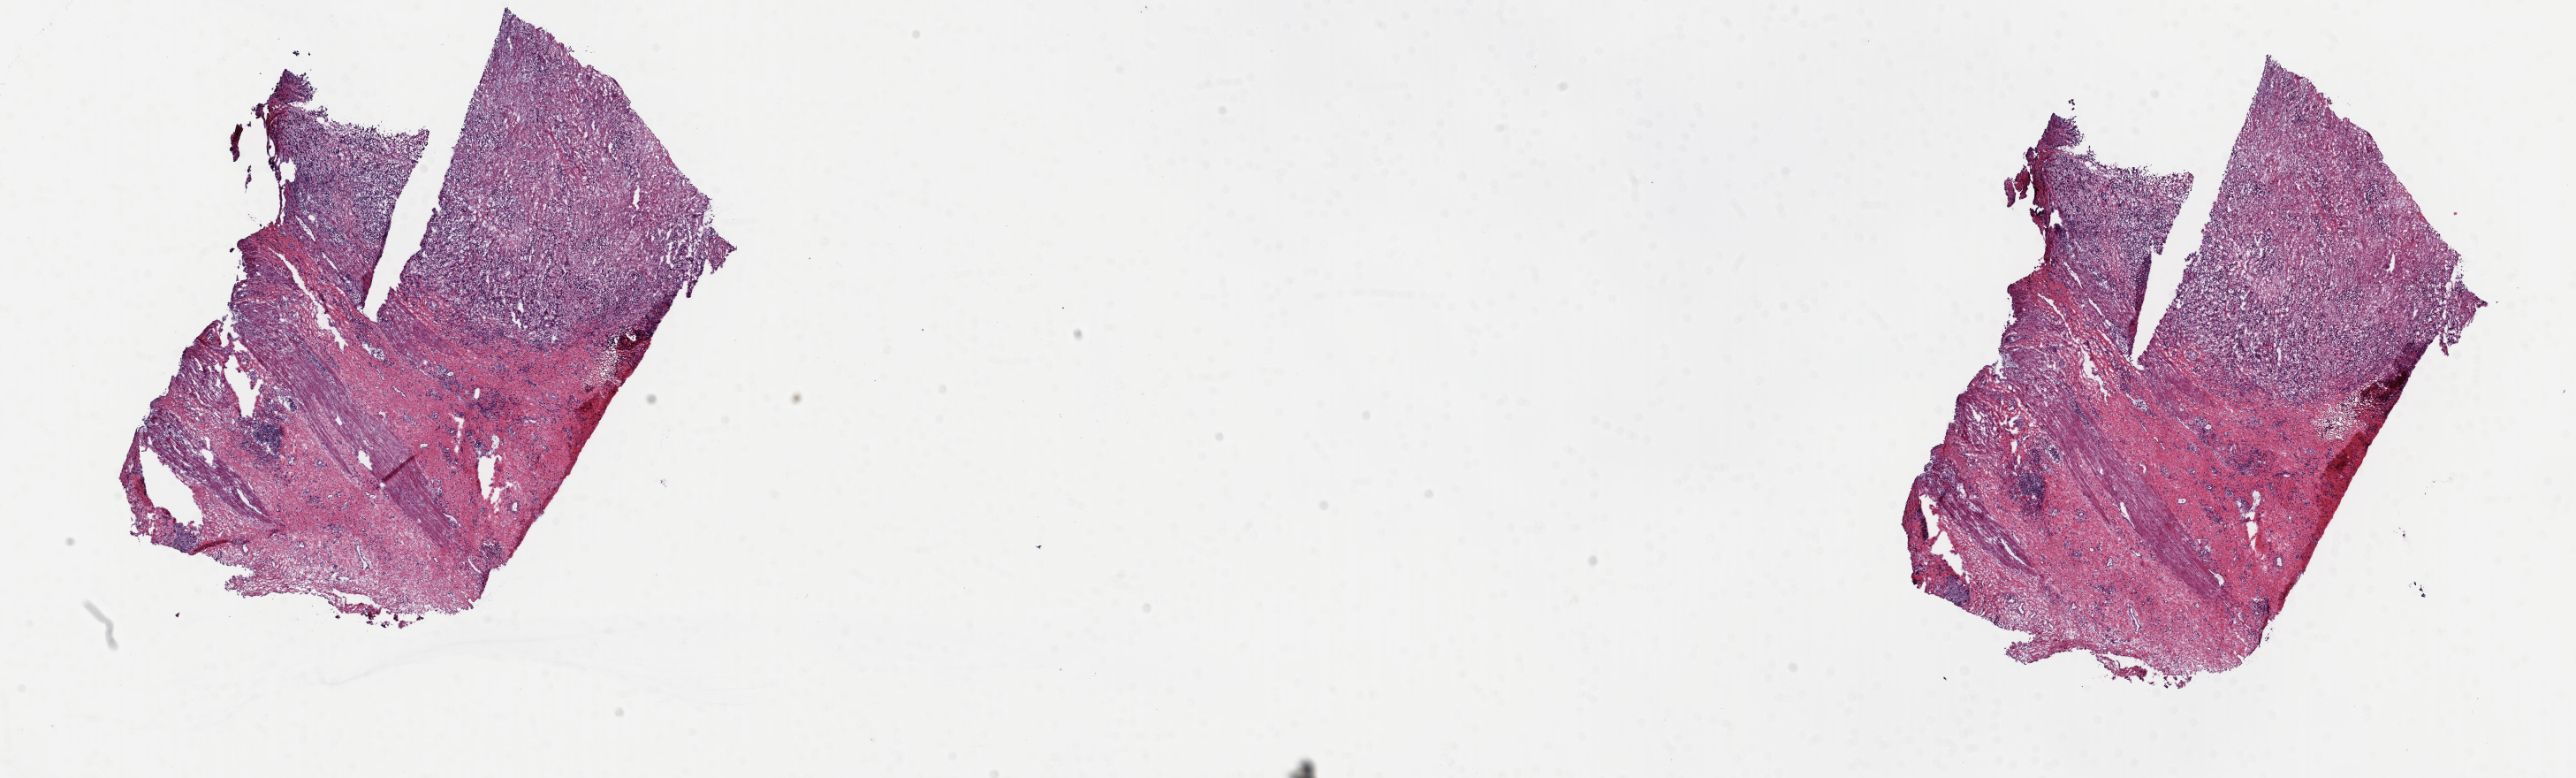
Digitized Hematoxylin and eosin (H&E) stained tissue section (whole slide) — shown as a low-resolution overview of the whole scanned area (about 23.0 x 7.0 mm, from a 40x scan). Frozen section from the top of the tissue portion. Sample: primary tumour, stomach. Patient: male, age at initial diagnosis 52 years. Histologic grade: G3 (poorly differentiated). Pathologist review of this section (percent, as recorded): tumour cells 25%, tumour nuclei 70%, normal cells 0%, stromal cells 62%, necrosis 13%. Infiltration values recorded for this section: lymphocyte infiltration 6%, monocyte infiltration 2%, neutrophil infiltration 2%.
• AJCC pathologic stage: IIIC (7th edition)
• lymph nodes positive (case pathology): 18 of 20 examined
• diagnosis: Carcinoma, diffuse type (fundus of stomach)